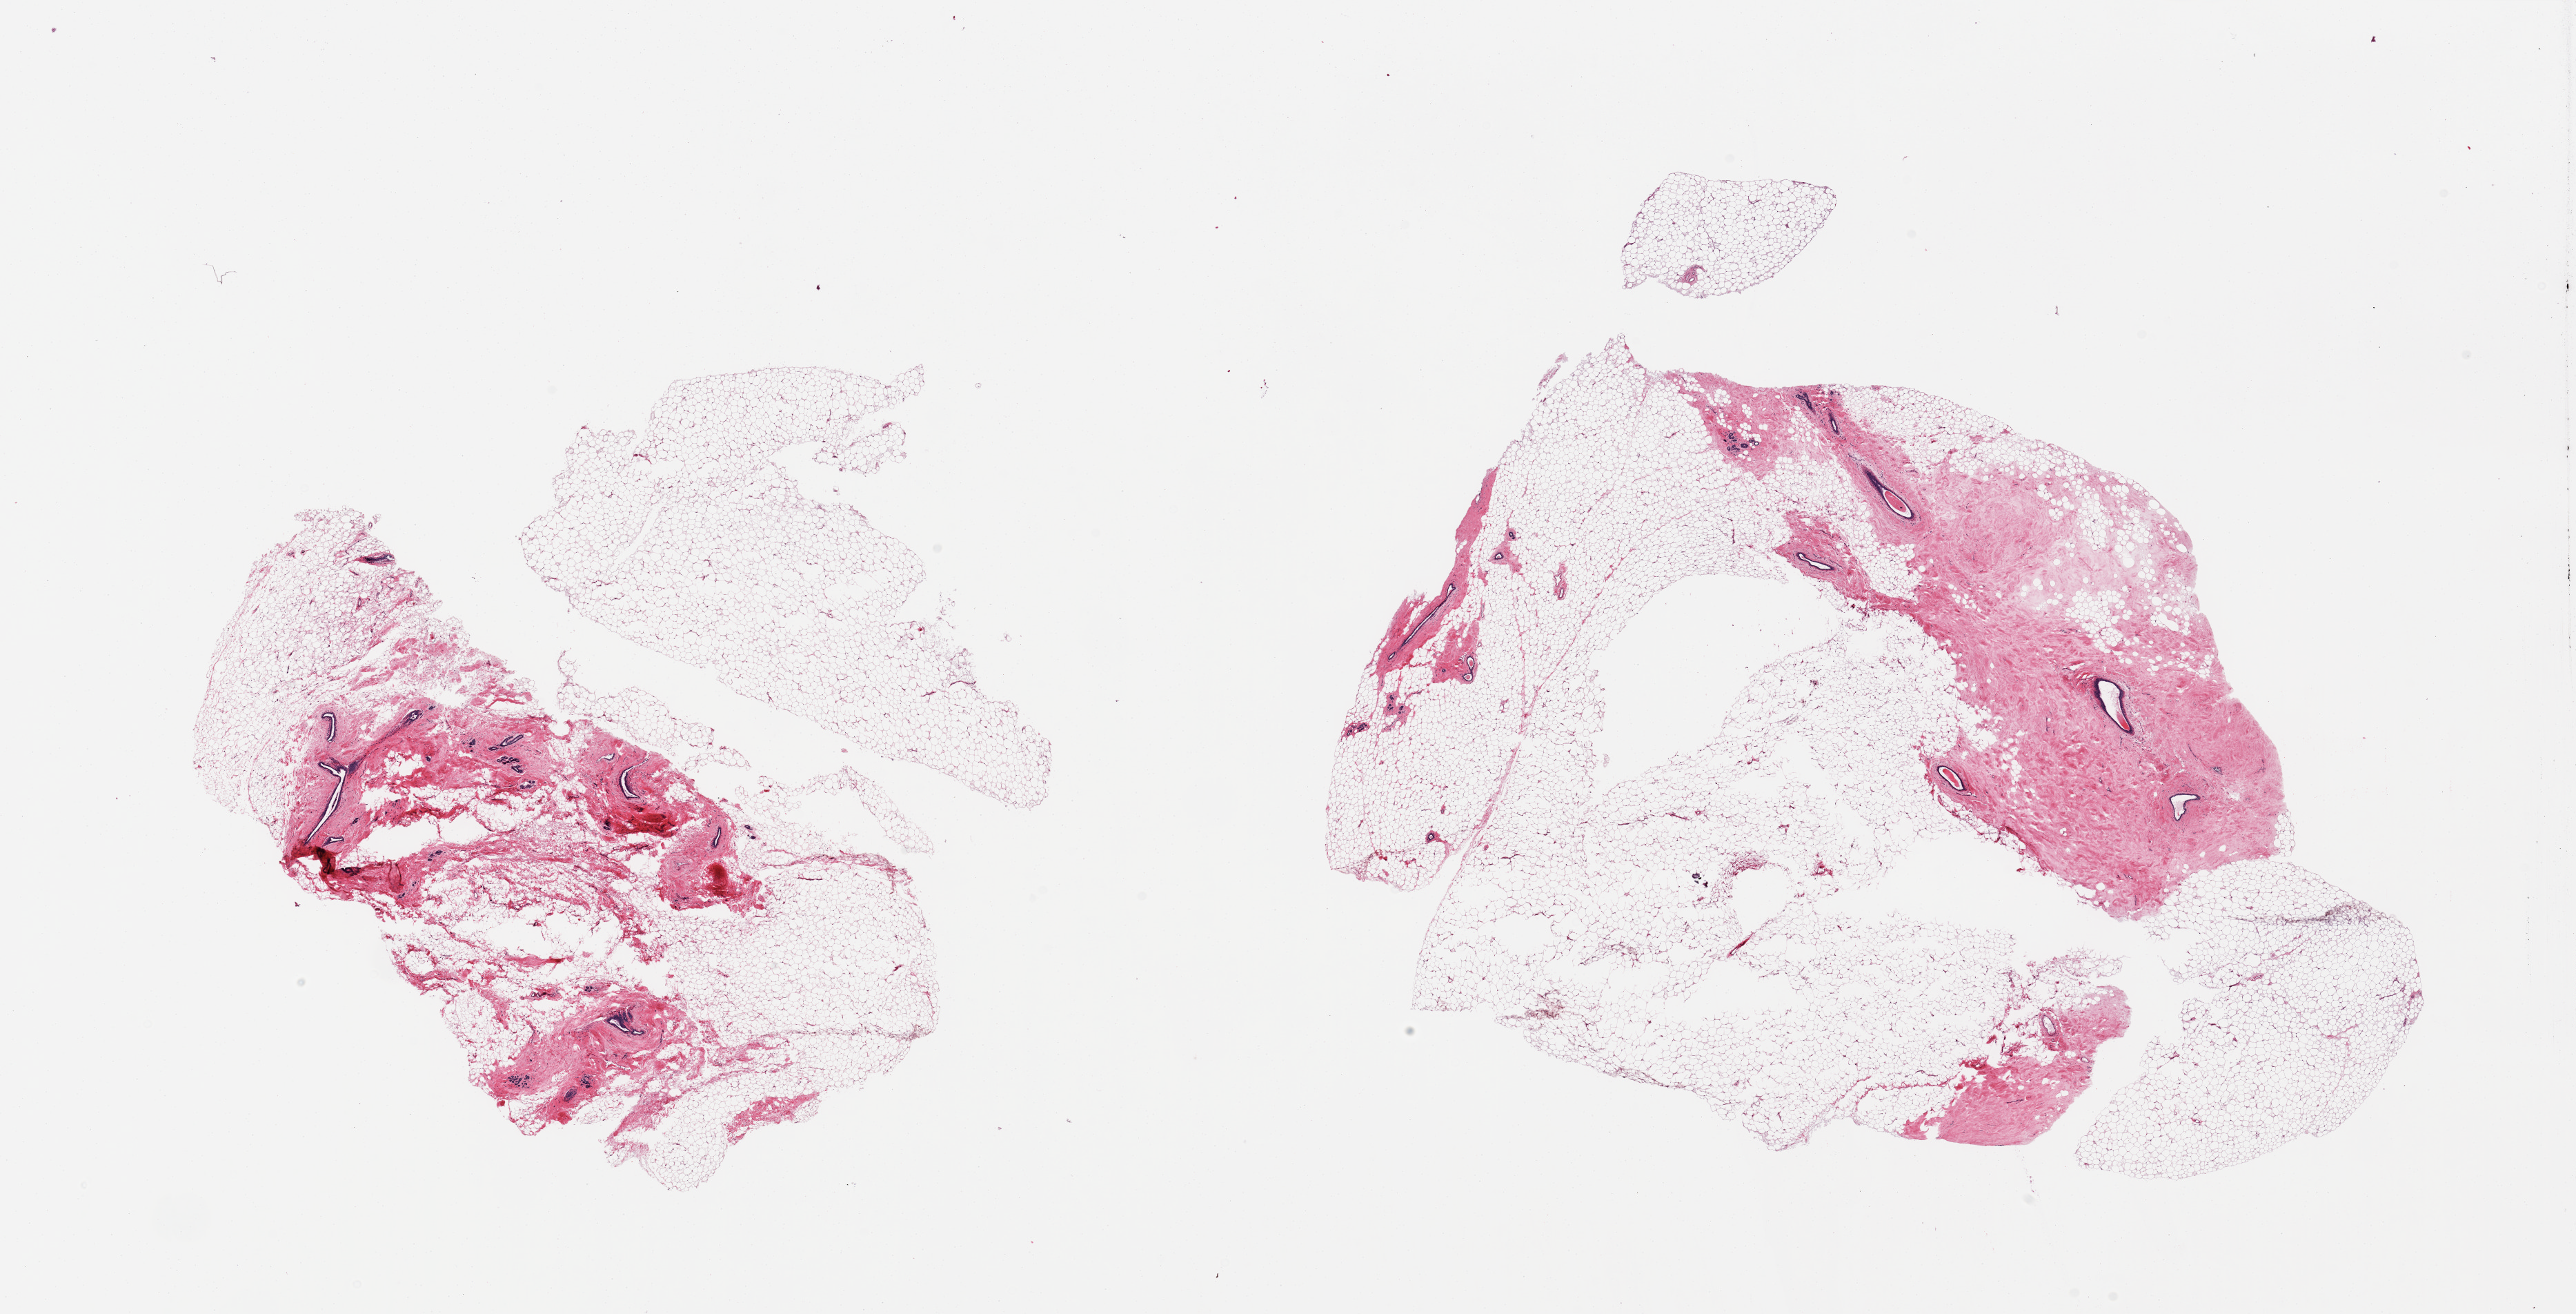
Whole-slide image, H&E stain, brightfield, low-resolution overview of the scanned area, about 29.5 x 15.1 mm (acquisition: 20x scan); PAXgene-fixed paraffin-embedded (PFPE) section; target tissue: breast; tissue donor sample. Donor sex: female.
Pathologist's review note for this sample: 2 pieces; 70% fat/30% dense fibrocollagenous stroma with benign ducts and lobules.